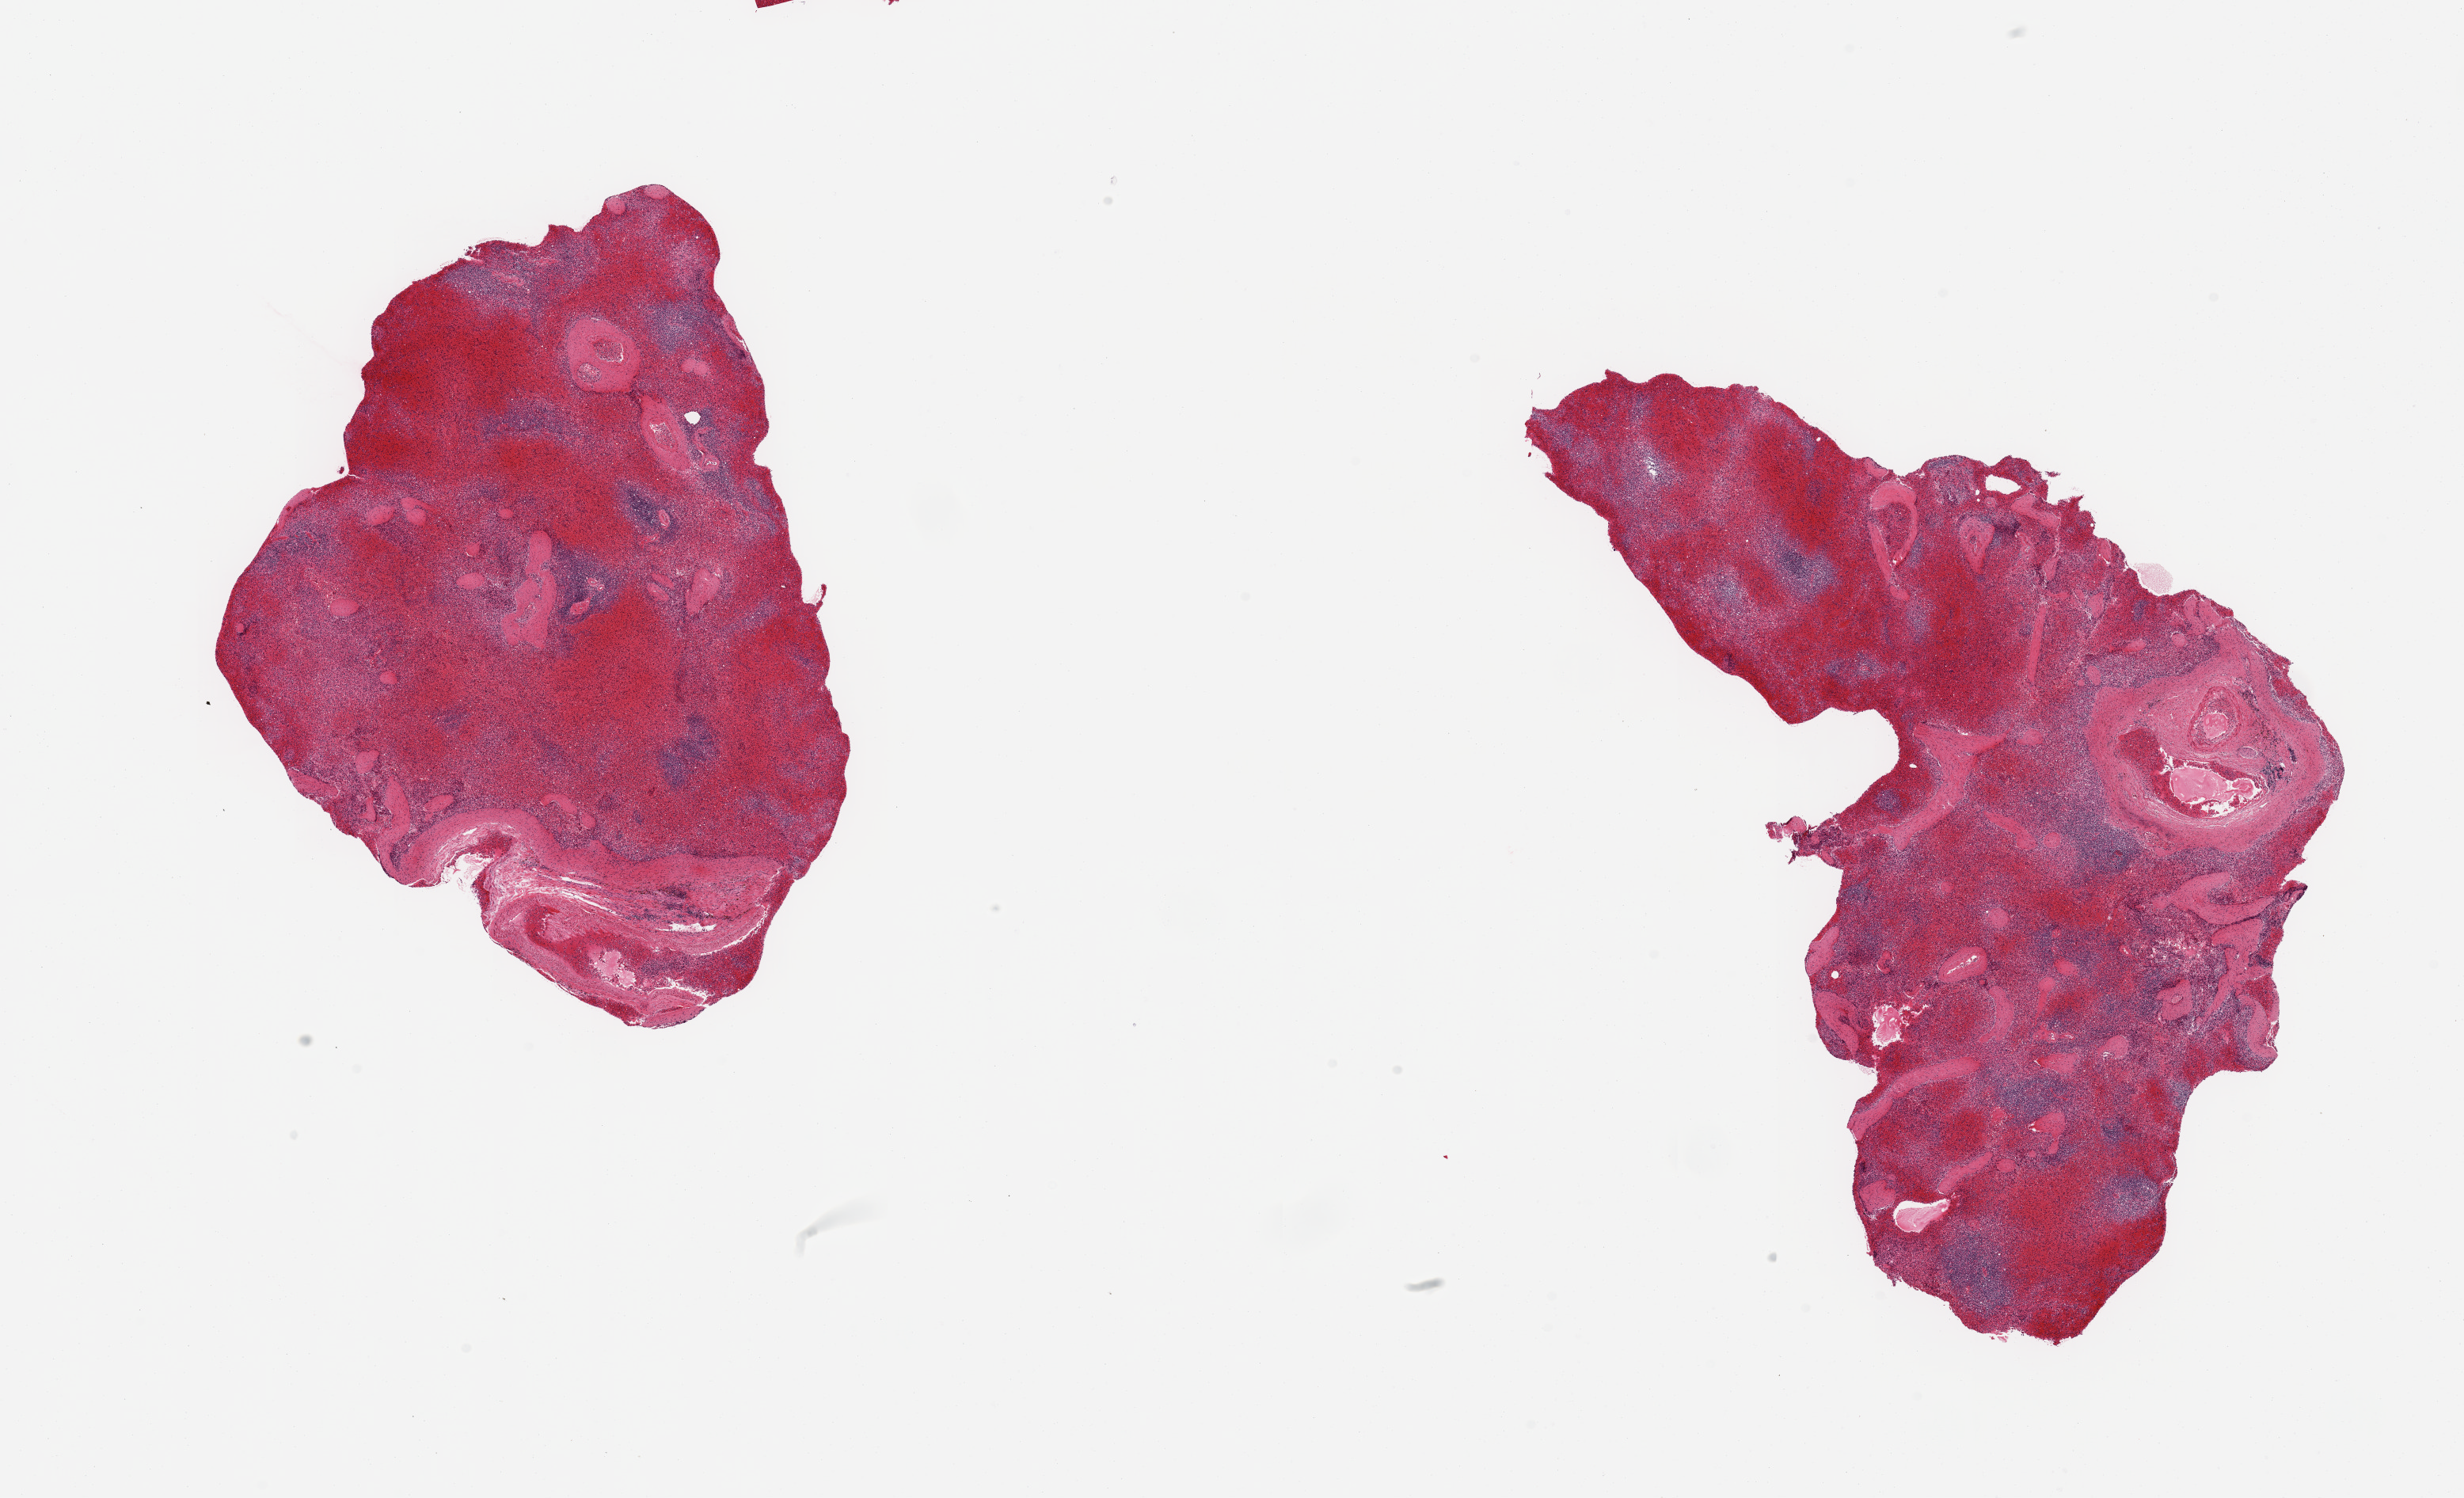
Whole-slide image, haematoxylin and eosin stain, a low-resolution overview of the entire scanned area, about 24.6 x 15.0 mm. PAXgene-fixed, paraffin-embedded tissue. Target tissue: spleen. Tissue donor sample. Donor: male.
Pathologist's review note for this sample: 2 pieces, moderate-severe congestion.